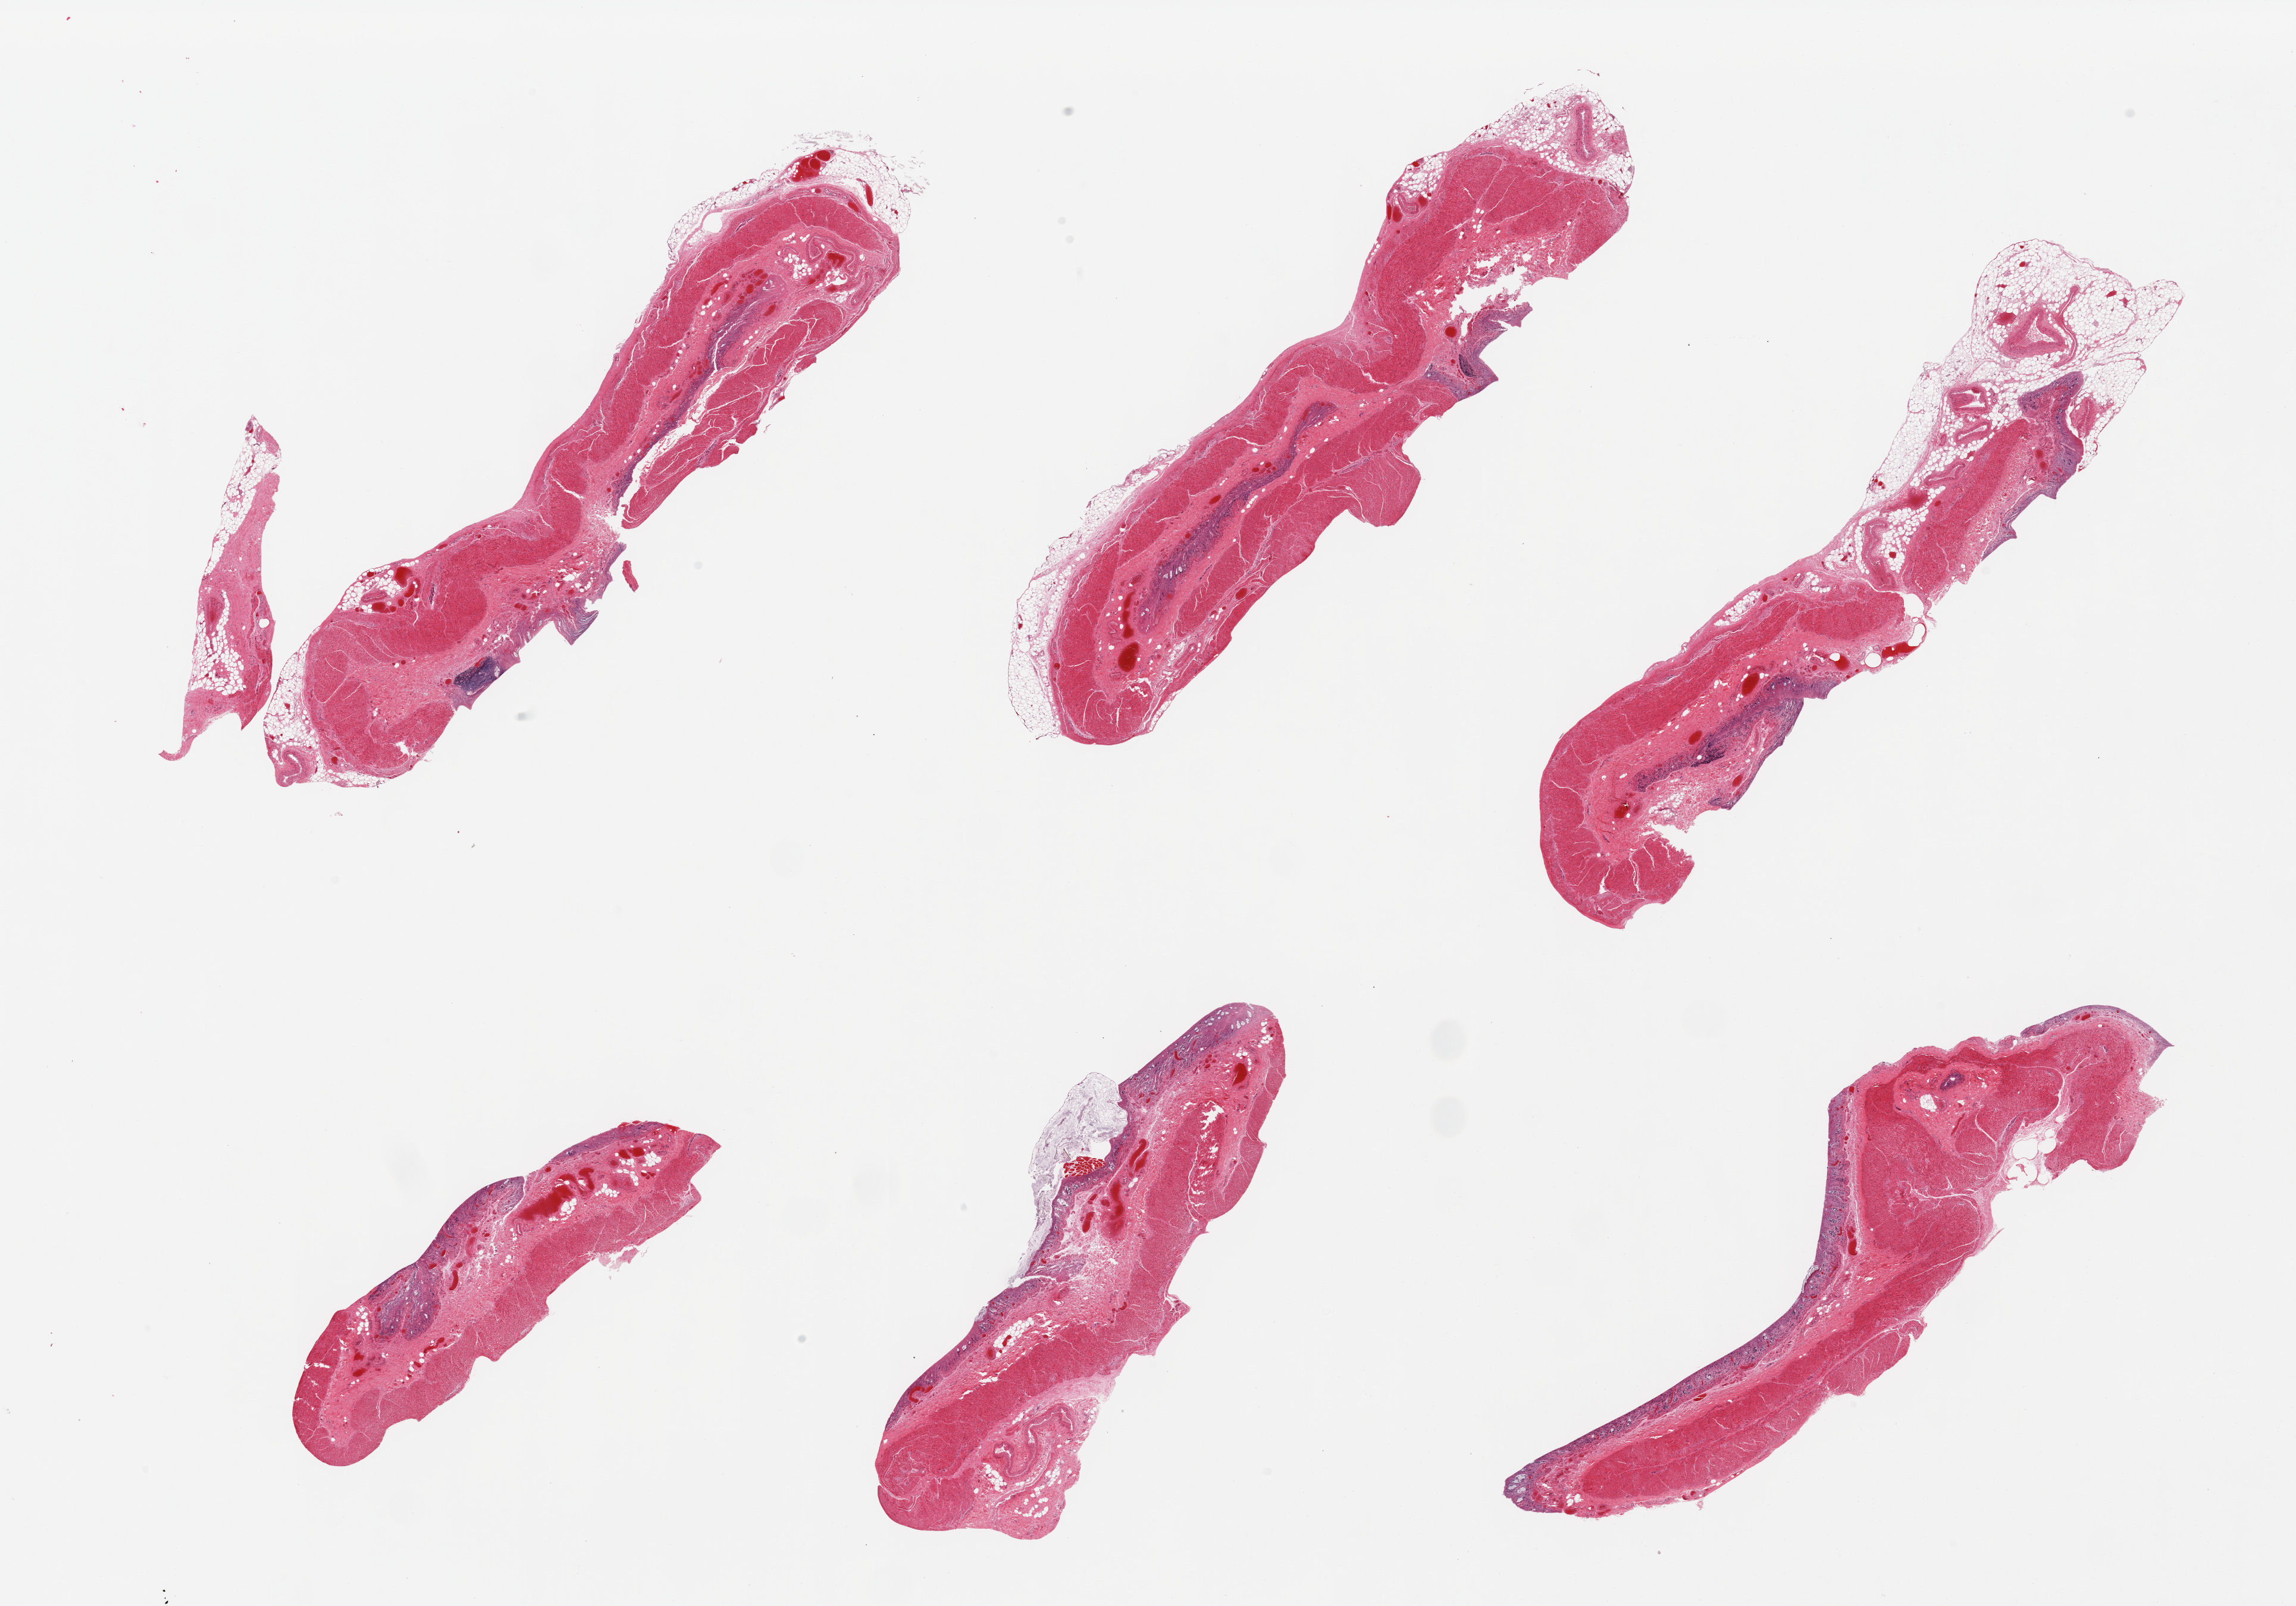
Digitized haematoxylin and eosin-stained section, brightfield, low-resolution overview of the scanned area, about 30.5 x 21.4 mm (from a 20x scan); PAXgene-fixed paraffin-embedded (PFPE) section; sampled site (target tissue): ileum; donor tissue sample. Male donor.
- review note (as recorded): 6 pieces; autolyzed mucosa with scant lymphoid component, muscularis (not target), contaminating fragment of skeletal muscle